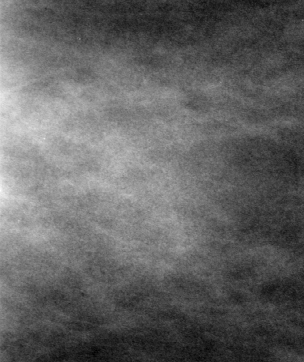
Region of interest cut from a scanned film mammogram (one marked finding); left breast; CC view; BI-RADS breast density category 2 (scale 1–4).
Marked abnormality: mass, shape oval, margins ill defined; BI-RADS assessment category 4; subtlety rating 4 on a 1 (subtle) to 5 (obvious) scale; pathology (as recorded): malignant.